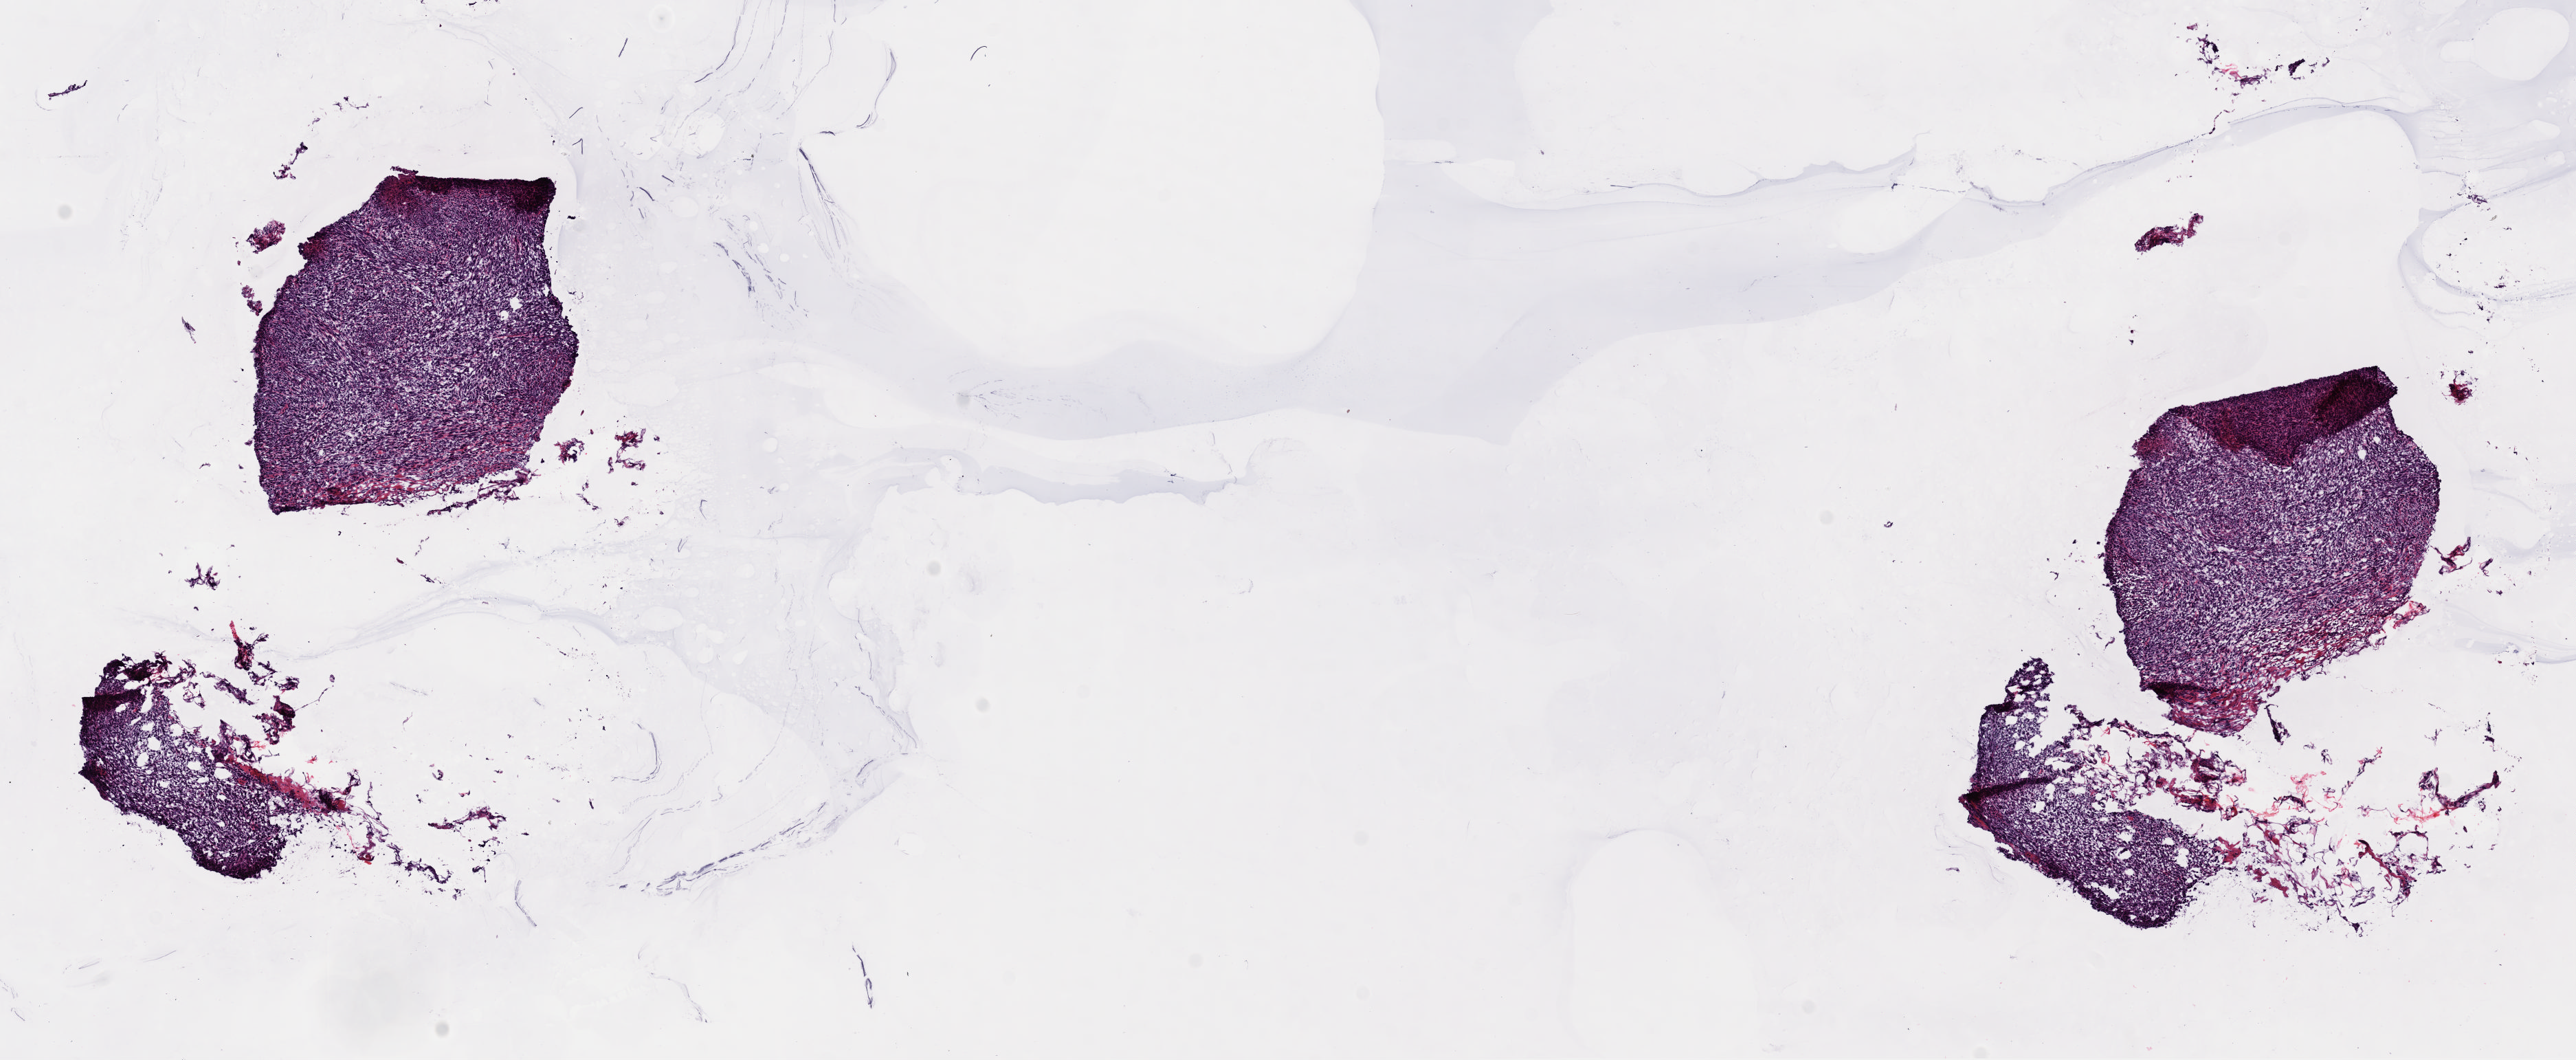
Digitized H&E-stained tissue section (whole slide), shown as a low-resolution overview of the whole scanned area (about 14.8 x 6.1 mm). Frozen section. Metastatic tumour sample. Male patient; age at initial diagnosis 54 years. Composition of this section per pathologist review: tumour cells 100%, tumour nuclei 95%, normal cells 0%, stromal cells 0%, necrosis 0%. Infiltration values recorded for this section: lymphocyte infiltration 0%, monocyte infiltration 0%, neutrophil infiltration 0%.
This section: metastatic tumour tissue. Patient diagnosis: Malignant melanoma, NOS.